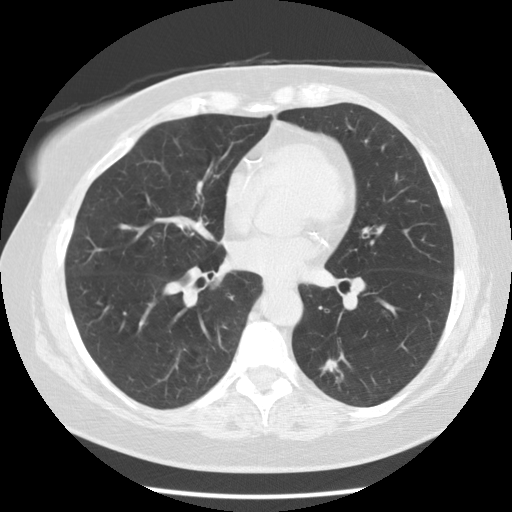
Chest CT (low-dose screening protocol), one axial image. Second screening round (one year after baseline). Lung window (W 1500 / L -600 HU). 2.5 mm slice thickness. Standard (soft-tissue) reconstruction kernel (STANDARD). 120 kVp. 512 × 512 image matrix, field of view 340 × 340 mm. Female, age 59 years at enrolment. Current smoker at enrolment.
Lesion marked by an expert reader, box from (x=298, y=342) to (x=369, y=408) px. The screening reader recorded 5 non-calcified nodules or masses ≥4 mm on this exam (right upper lobe, right lower lobe, right lower lobe, left lower lobe, left lower lobe); which of them this box marks is not recorded. Participant outcome: lung cancer diagnosed 343 days after this screen (after the third annual screen) — adenocarcinoma, NOS, left lower lobe, poorly differentiated (G3), stage IA (AJCC 6th edition), 15 mm at pathology.